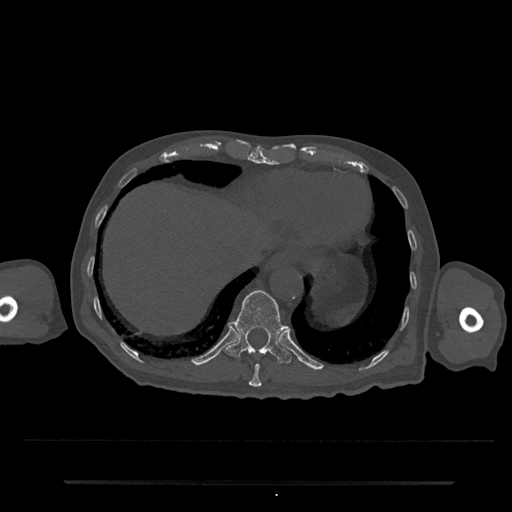
CT including the spine, one axial slice; position 268 of 797 along the scan axis; reconstruction kernel Br40s/3; 120 kVp; bone window (W 1800 / L 400 HU); 0.5 mm slice thickness; 512 × 512 image matrix, field of view 427 × 427 mm. Patient: male, 74 years. Case-level facts recorded for this patient, not image findings: primary cancer: prostate.
Structures marked on this image (semi-automatically segmented with operator editing):
- T10 vertebra: bounding box [x1, y1, x2, y2] px = [249, 364, 262, 388]
- T11 vertebra: [225, 290, 292, 365]